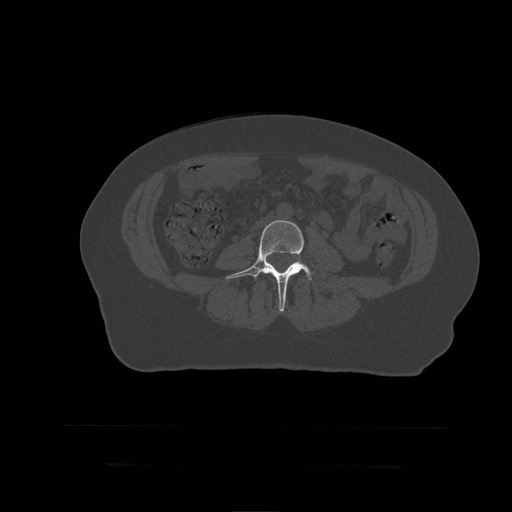
CT including the spine, one axial slice. Slice 98 of 399 in the series (ordered by position). Reconstruction kernel STANDARD. 120 kVp. Bone window (W 1800 / L 400 HU). 1.25 mm slice thickness. 512 × 512 image matrix. Patient age 41 years. Case-level facts recorded for this patient, not image findings: primary cancer: breast.
Structures marked on this image (semi-automatic segmentation, software-assisted and operator-edited):
- L4 vertebra: bounding box [x1, y1, x2, y2] px = [226, 220, 315, 312]